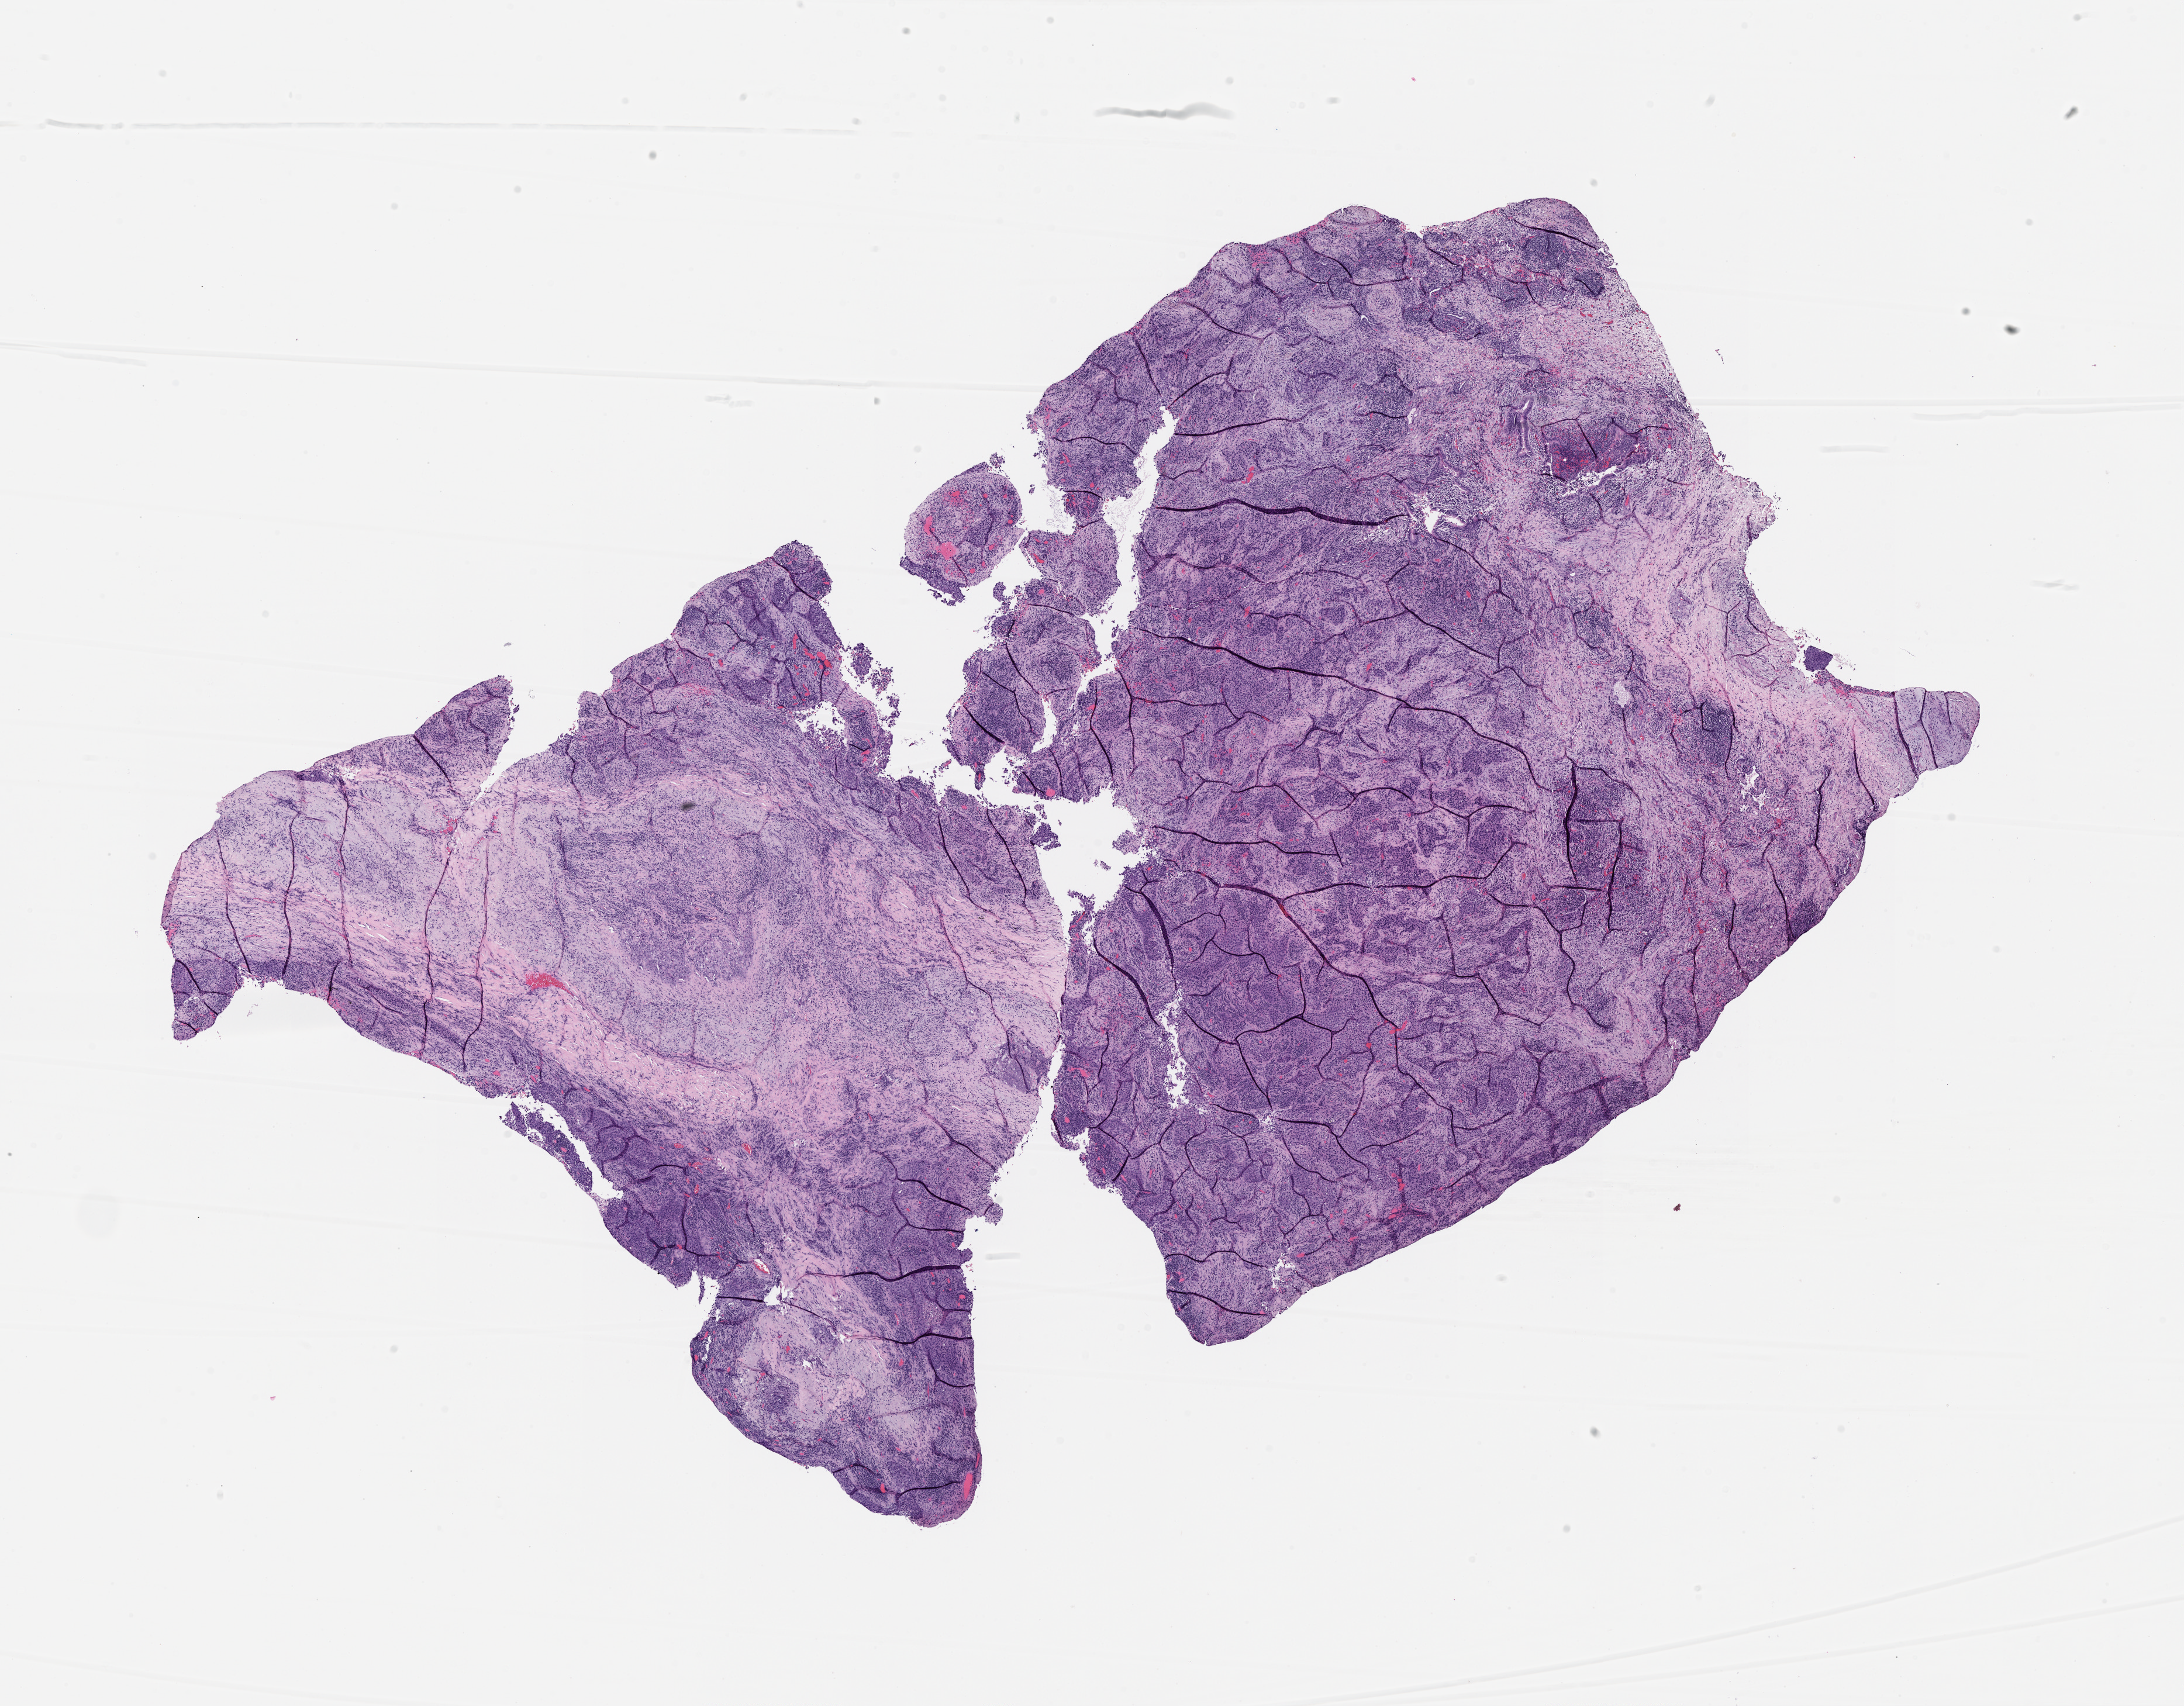
Digitized H&E tissue section (whole slide) — low-resolution overview of the scanned area, about 15.0 x 11.7 mm (slide scanned at 20x), lung, tumour tissue. Female, 82 y/o.
Patient diagnosis (cohort enrolment): squamous cell carcinoma (lung).